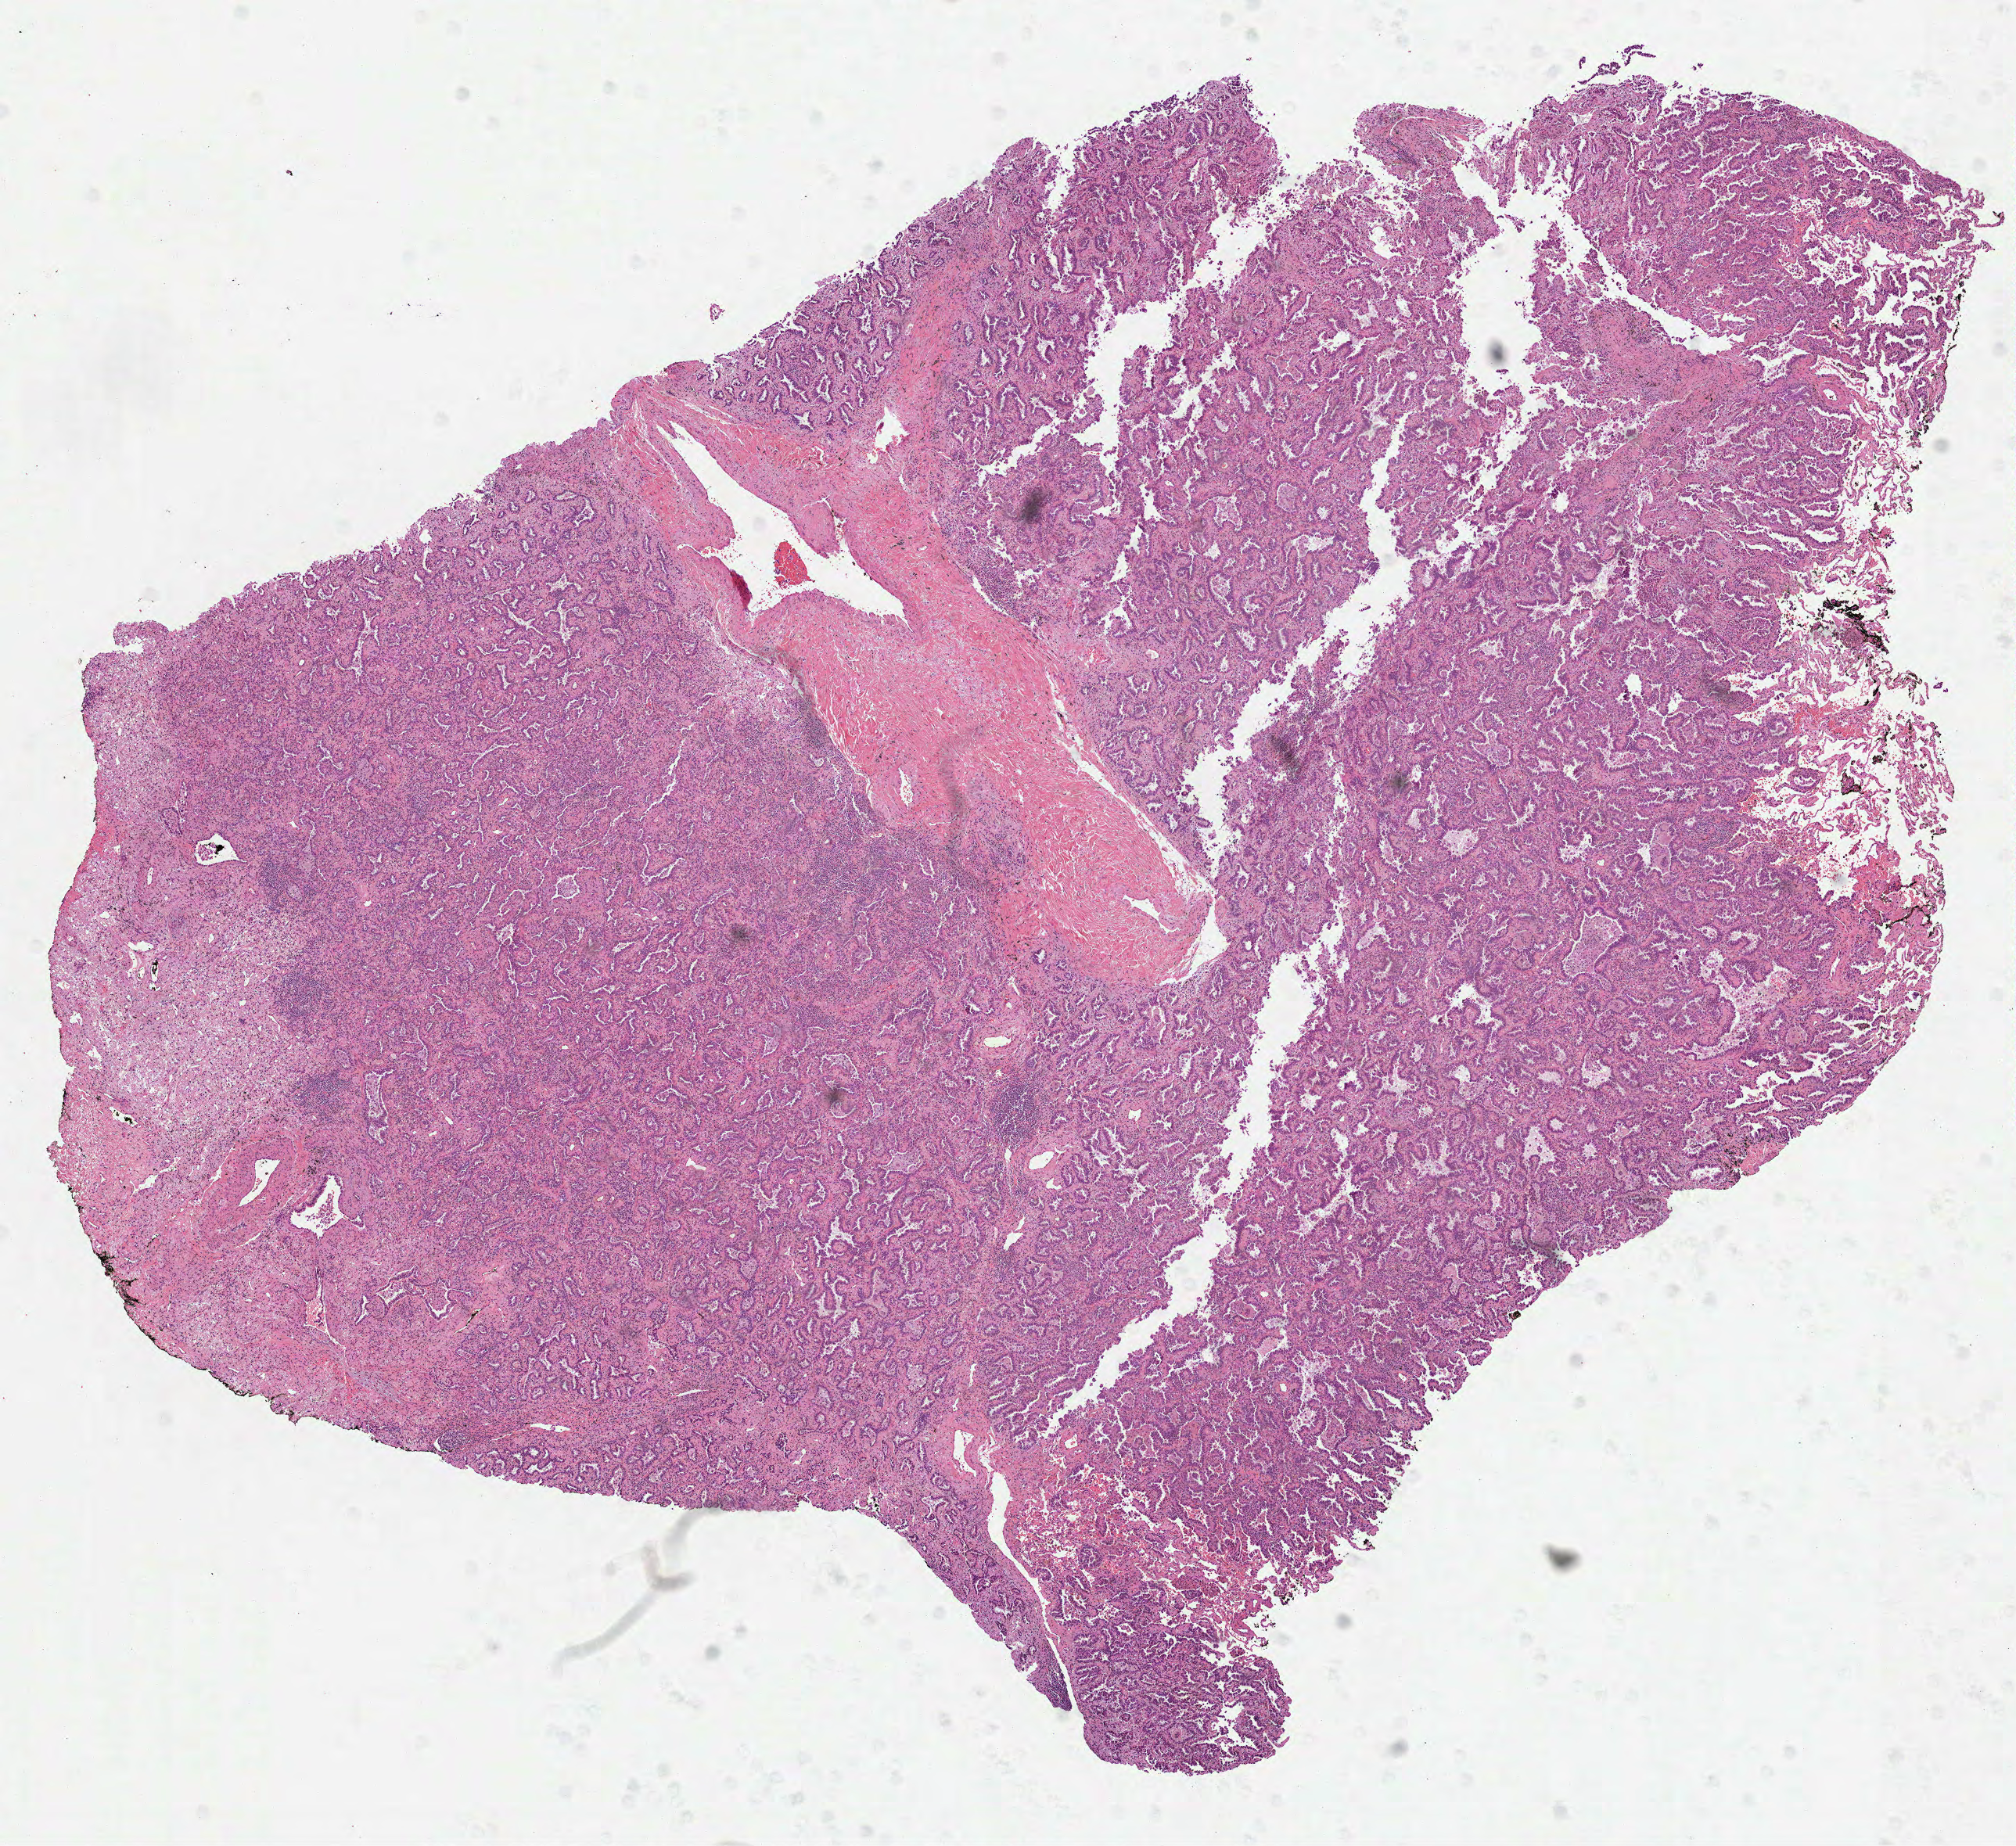
H&E whole-slide image — a low-resolution overview of the entire scanned area, about 10.4 x 9.5 mm. Formalin-fixed paraffin-embedded (FFPE) diagnostic section. Lung, primary tumour sample. Female, age 59 years at initial diagnosis.
Diagnosis: Adenocarcinoma, NOS (upper lobe, lung).